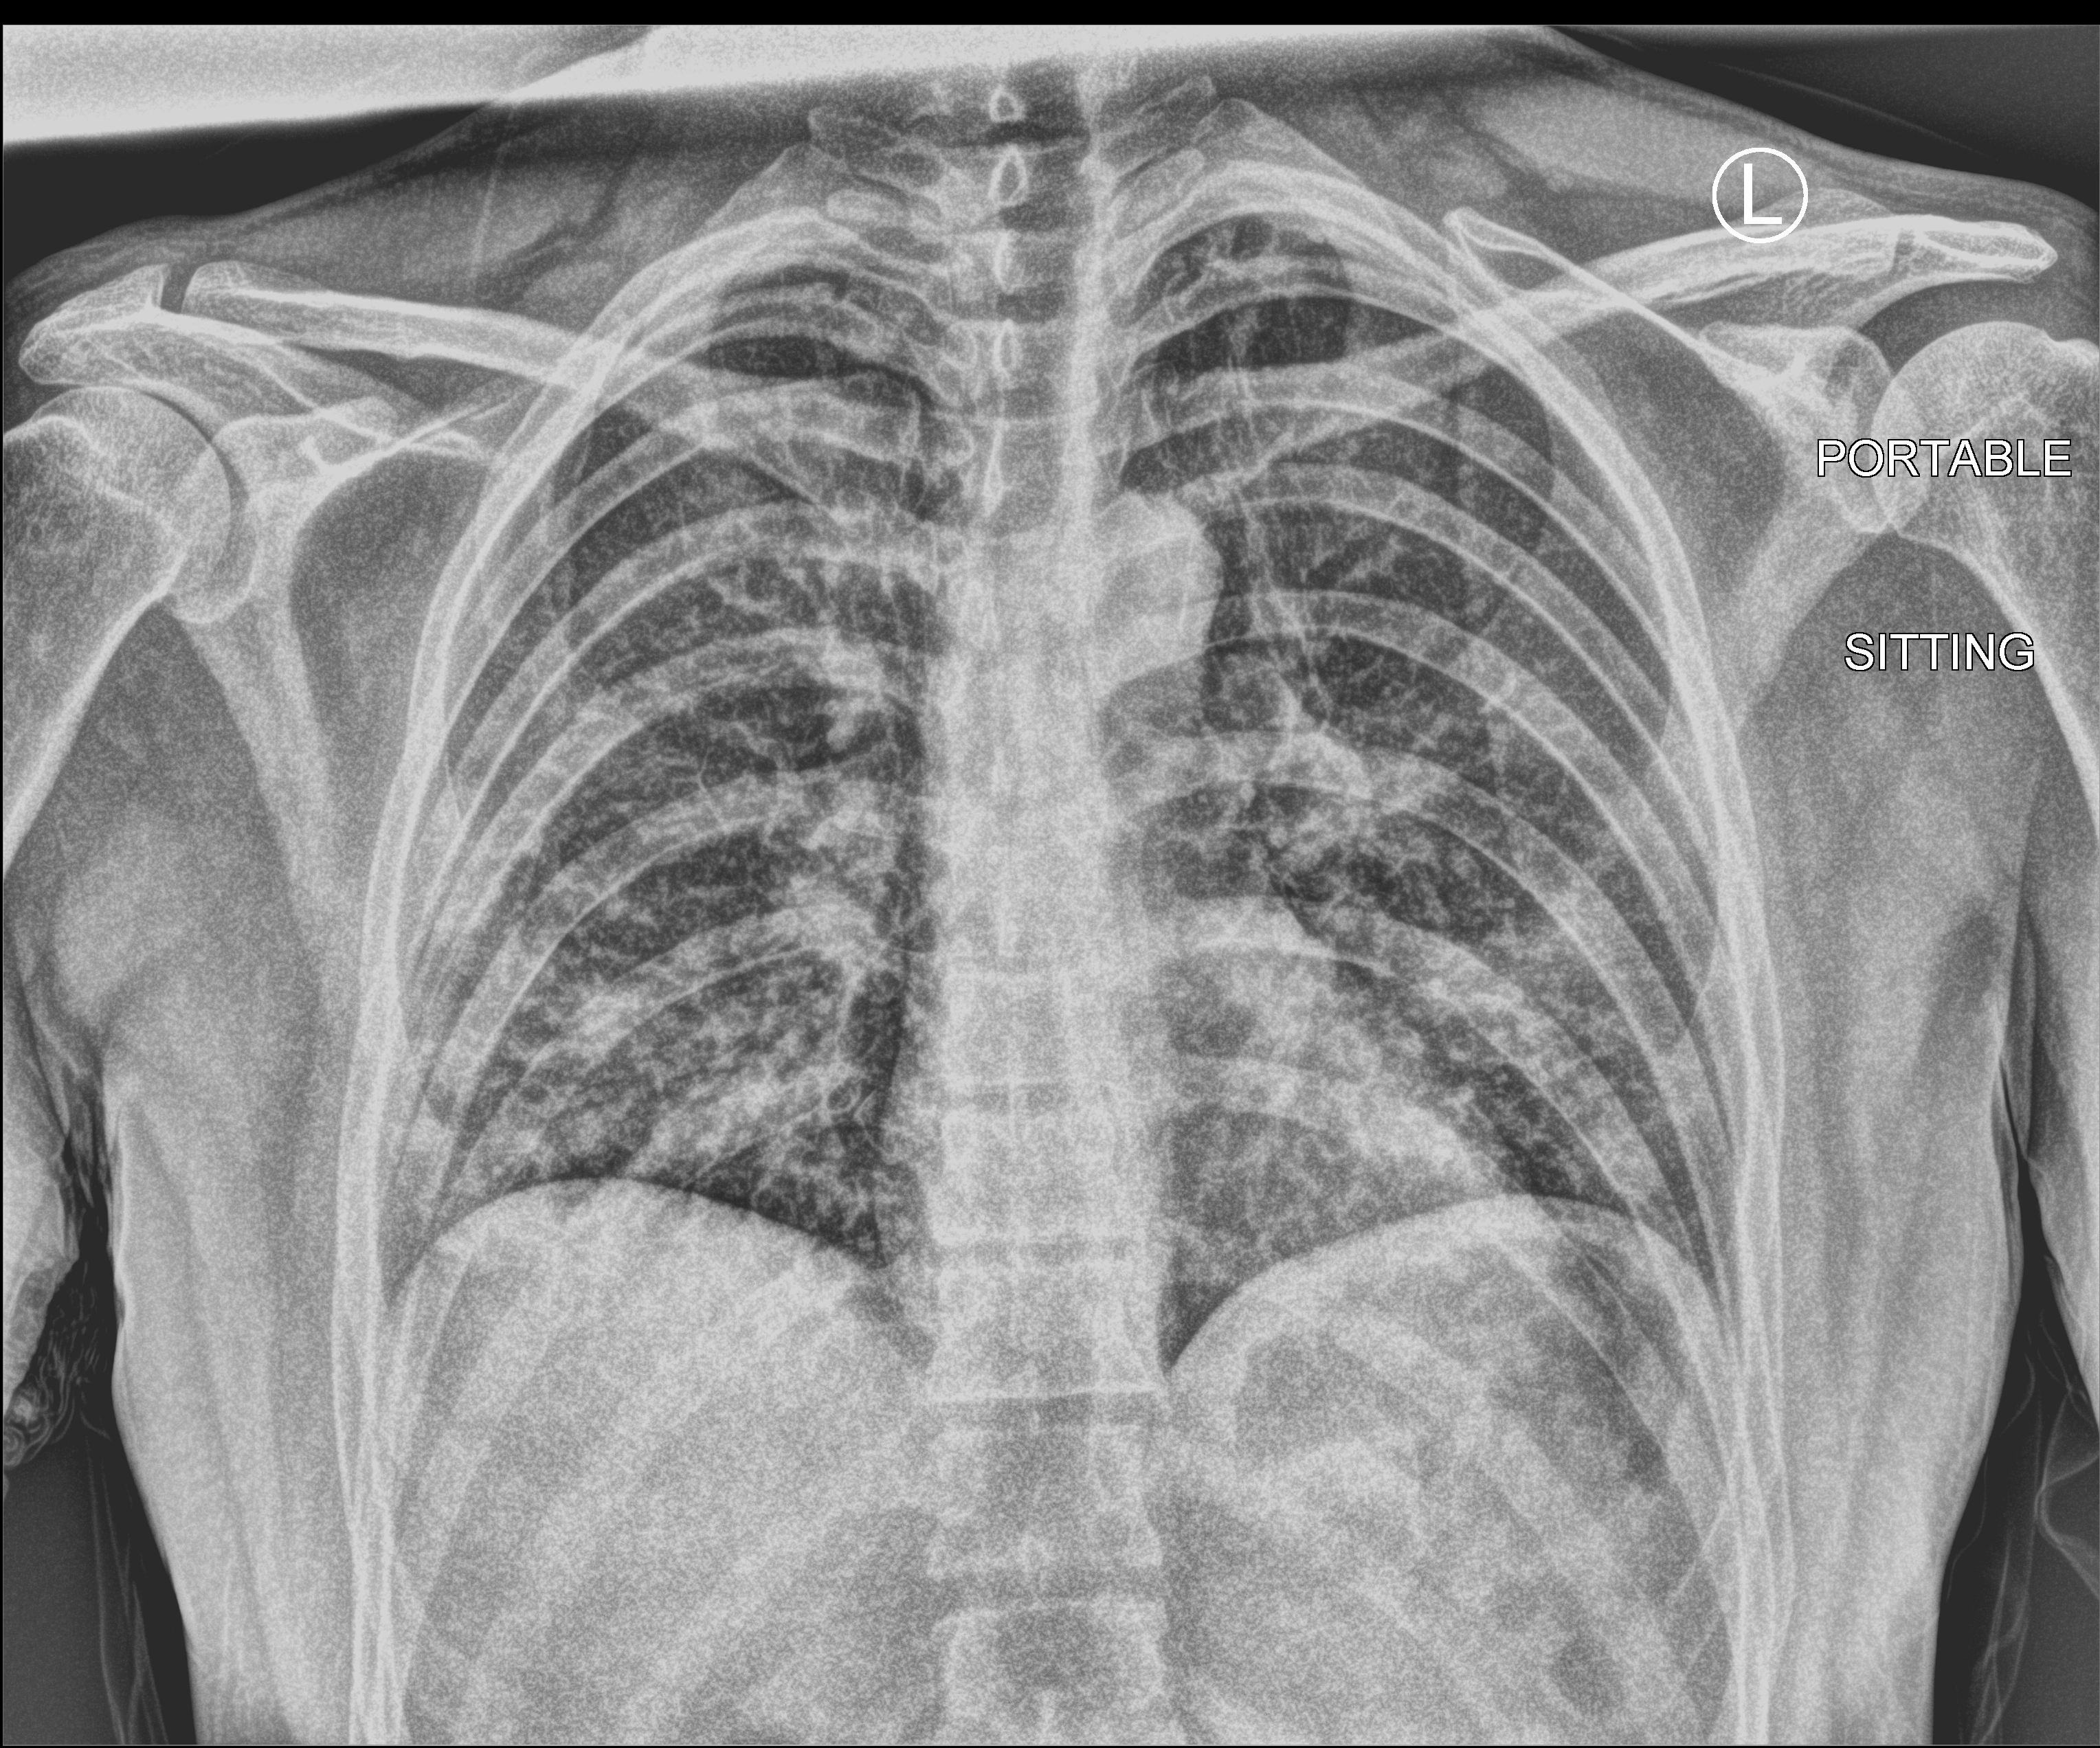
Chest X-ray (portable). Male patient hospitalised with COVID-19, age 18–59 years.
From the hospital-stay record, not from the radiograph (when in the stay this image was taken is not recorded):
- admitted to intensive care during this hospital stay: no
- mechanically ventilated during this hospital stay: no